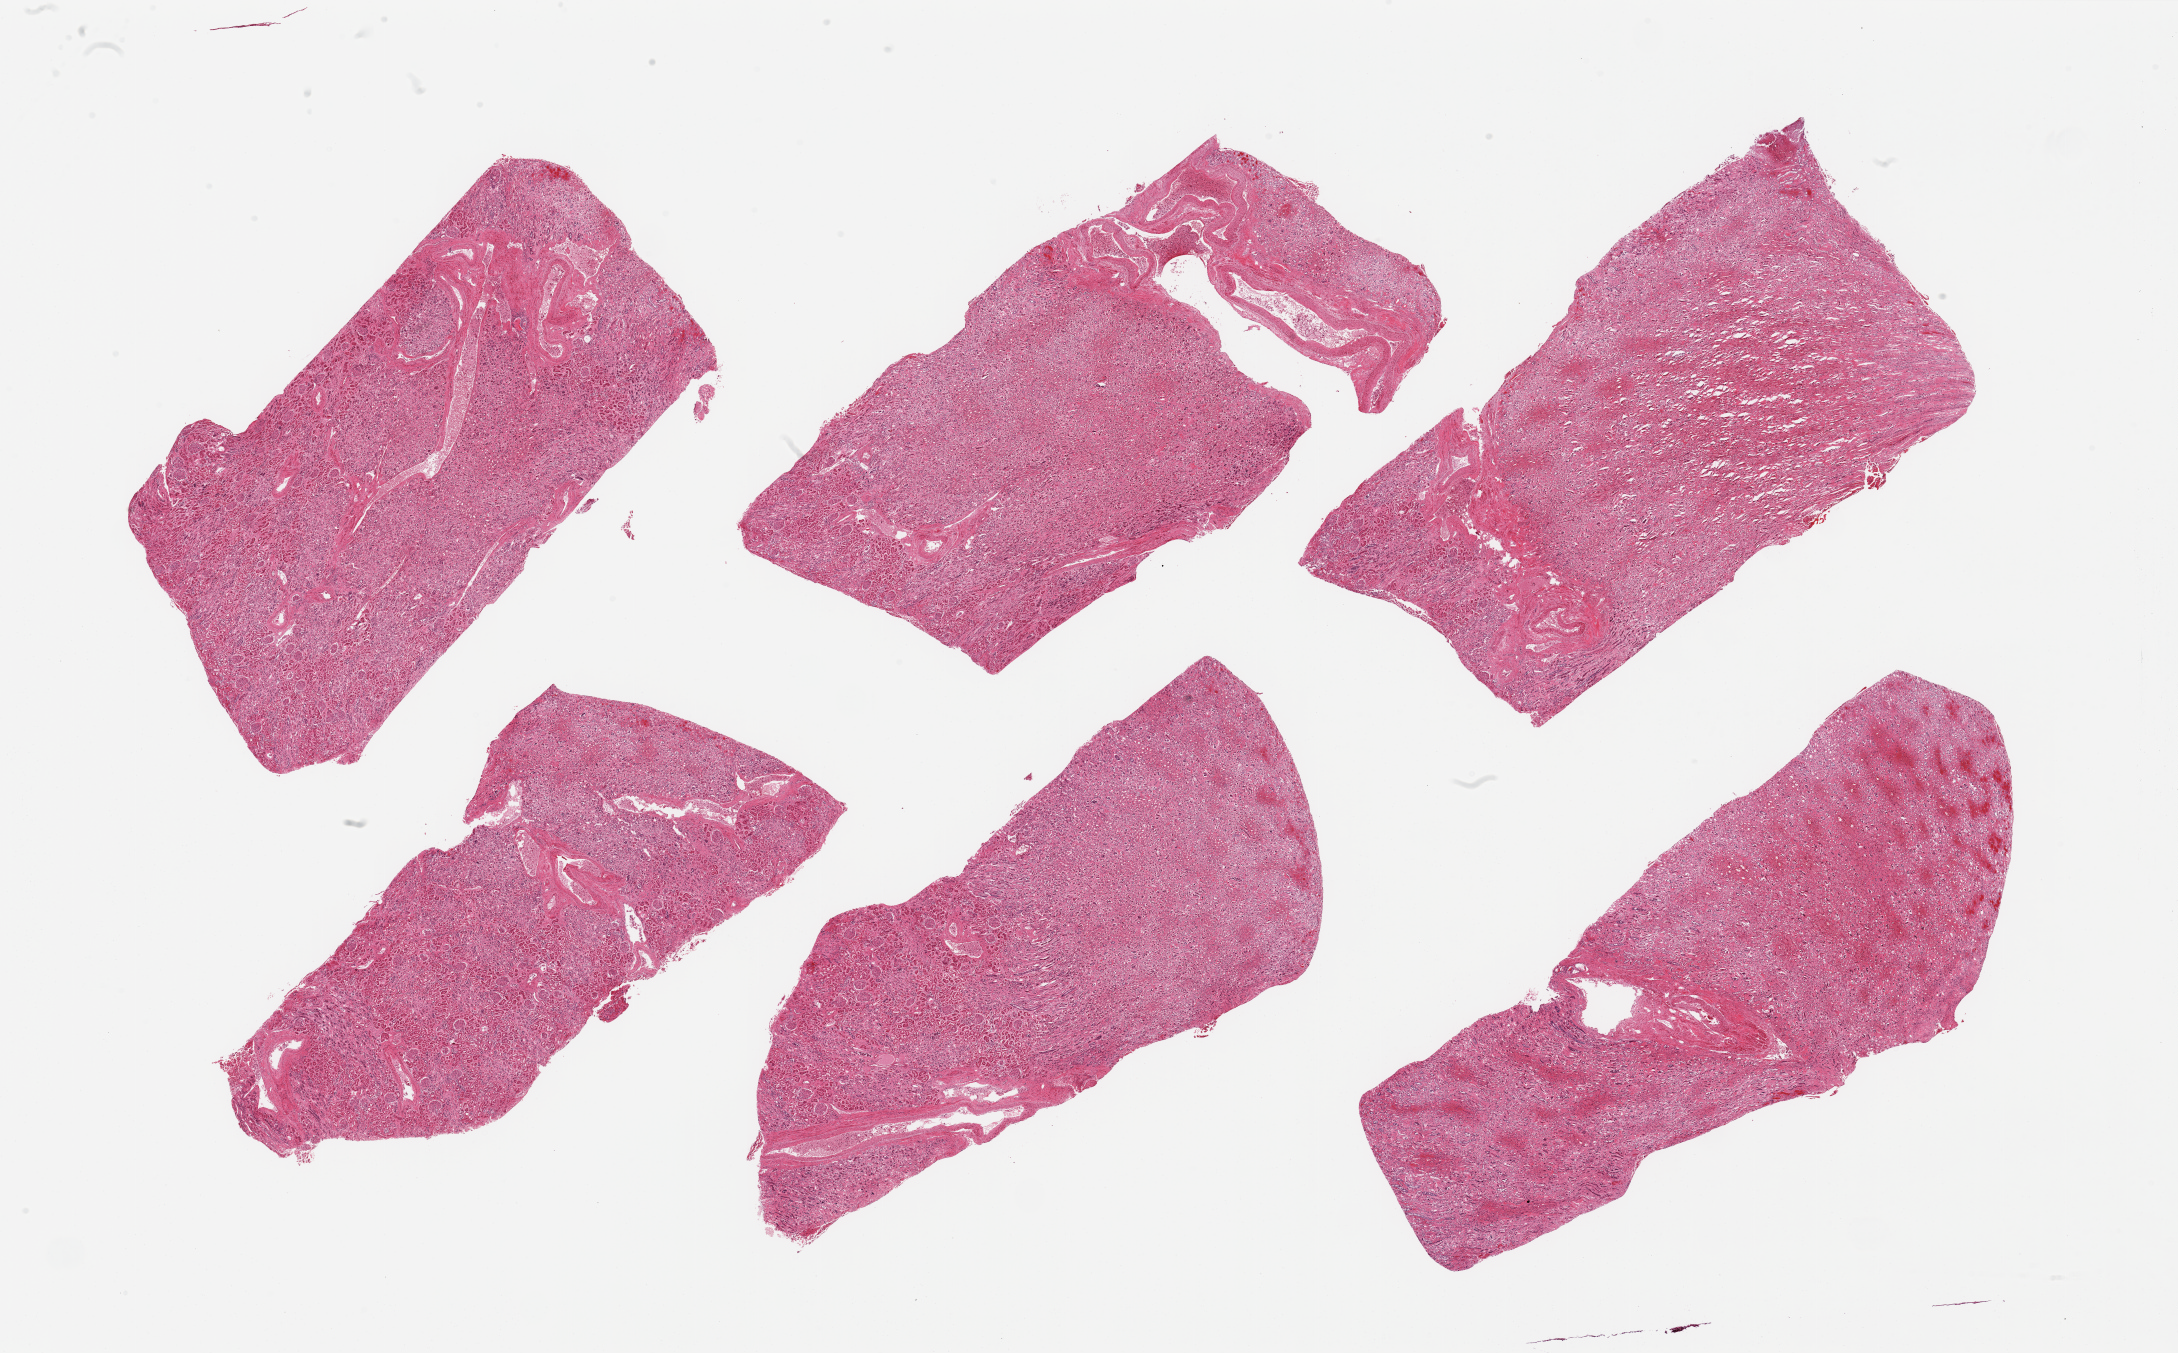
Haematoxylin and eosin whole-slide image, a low-resolution overview of the entire scanned area, about 34.5 x 21.4 mm (slide scanned at 20x); PAXgene-fixed paraffin-embedded (PFPE) section; sampled site (target tissue): renal cortex; tissue donor sample. Donor: male.
Review note (as recorded): 6 pieces, glomeruli present, tubules with advanced autolysis.